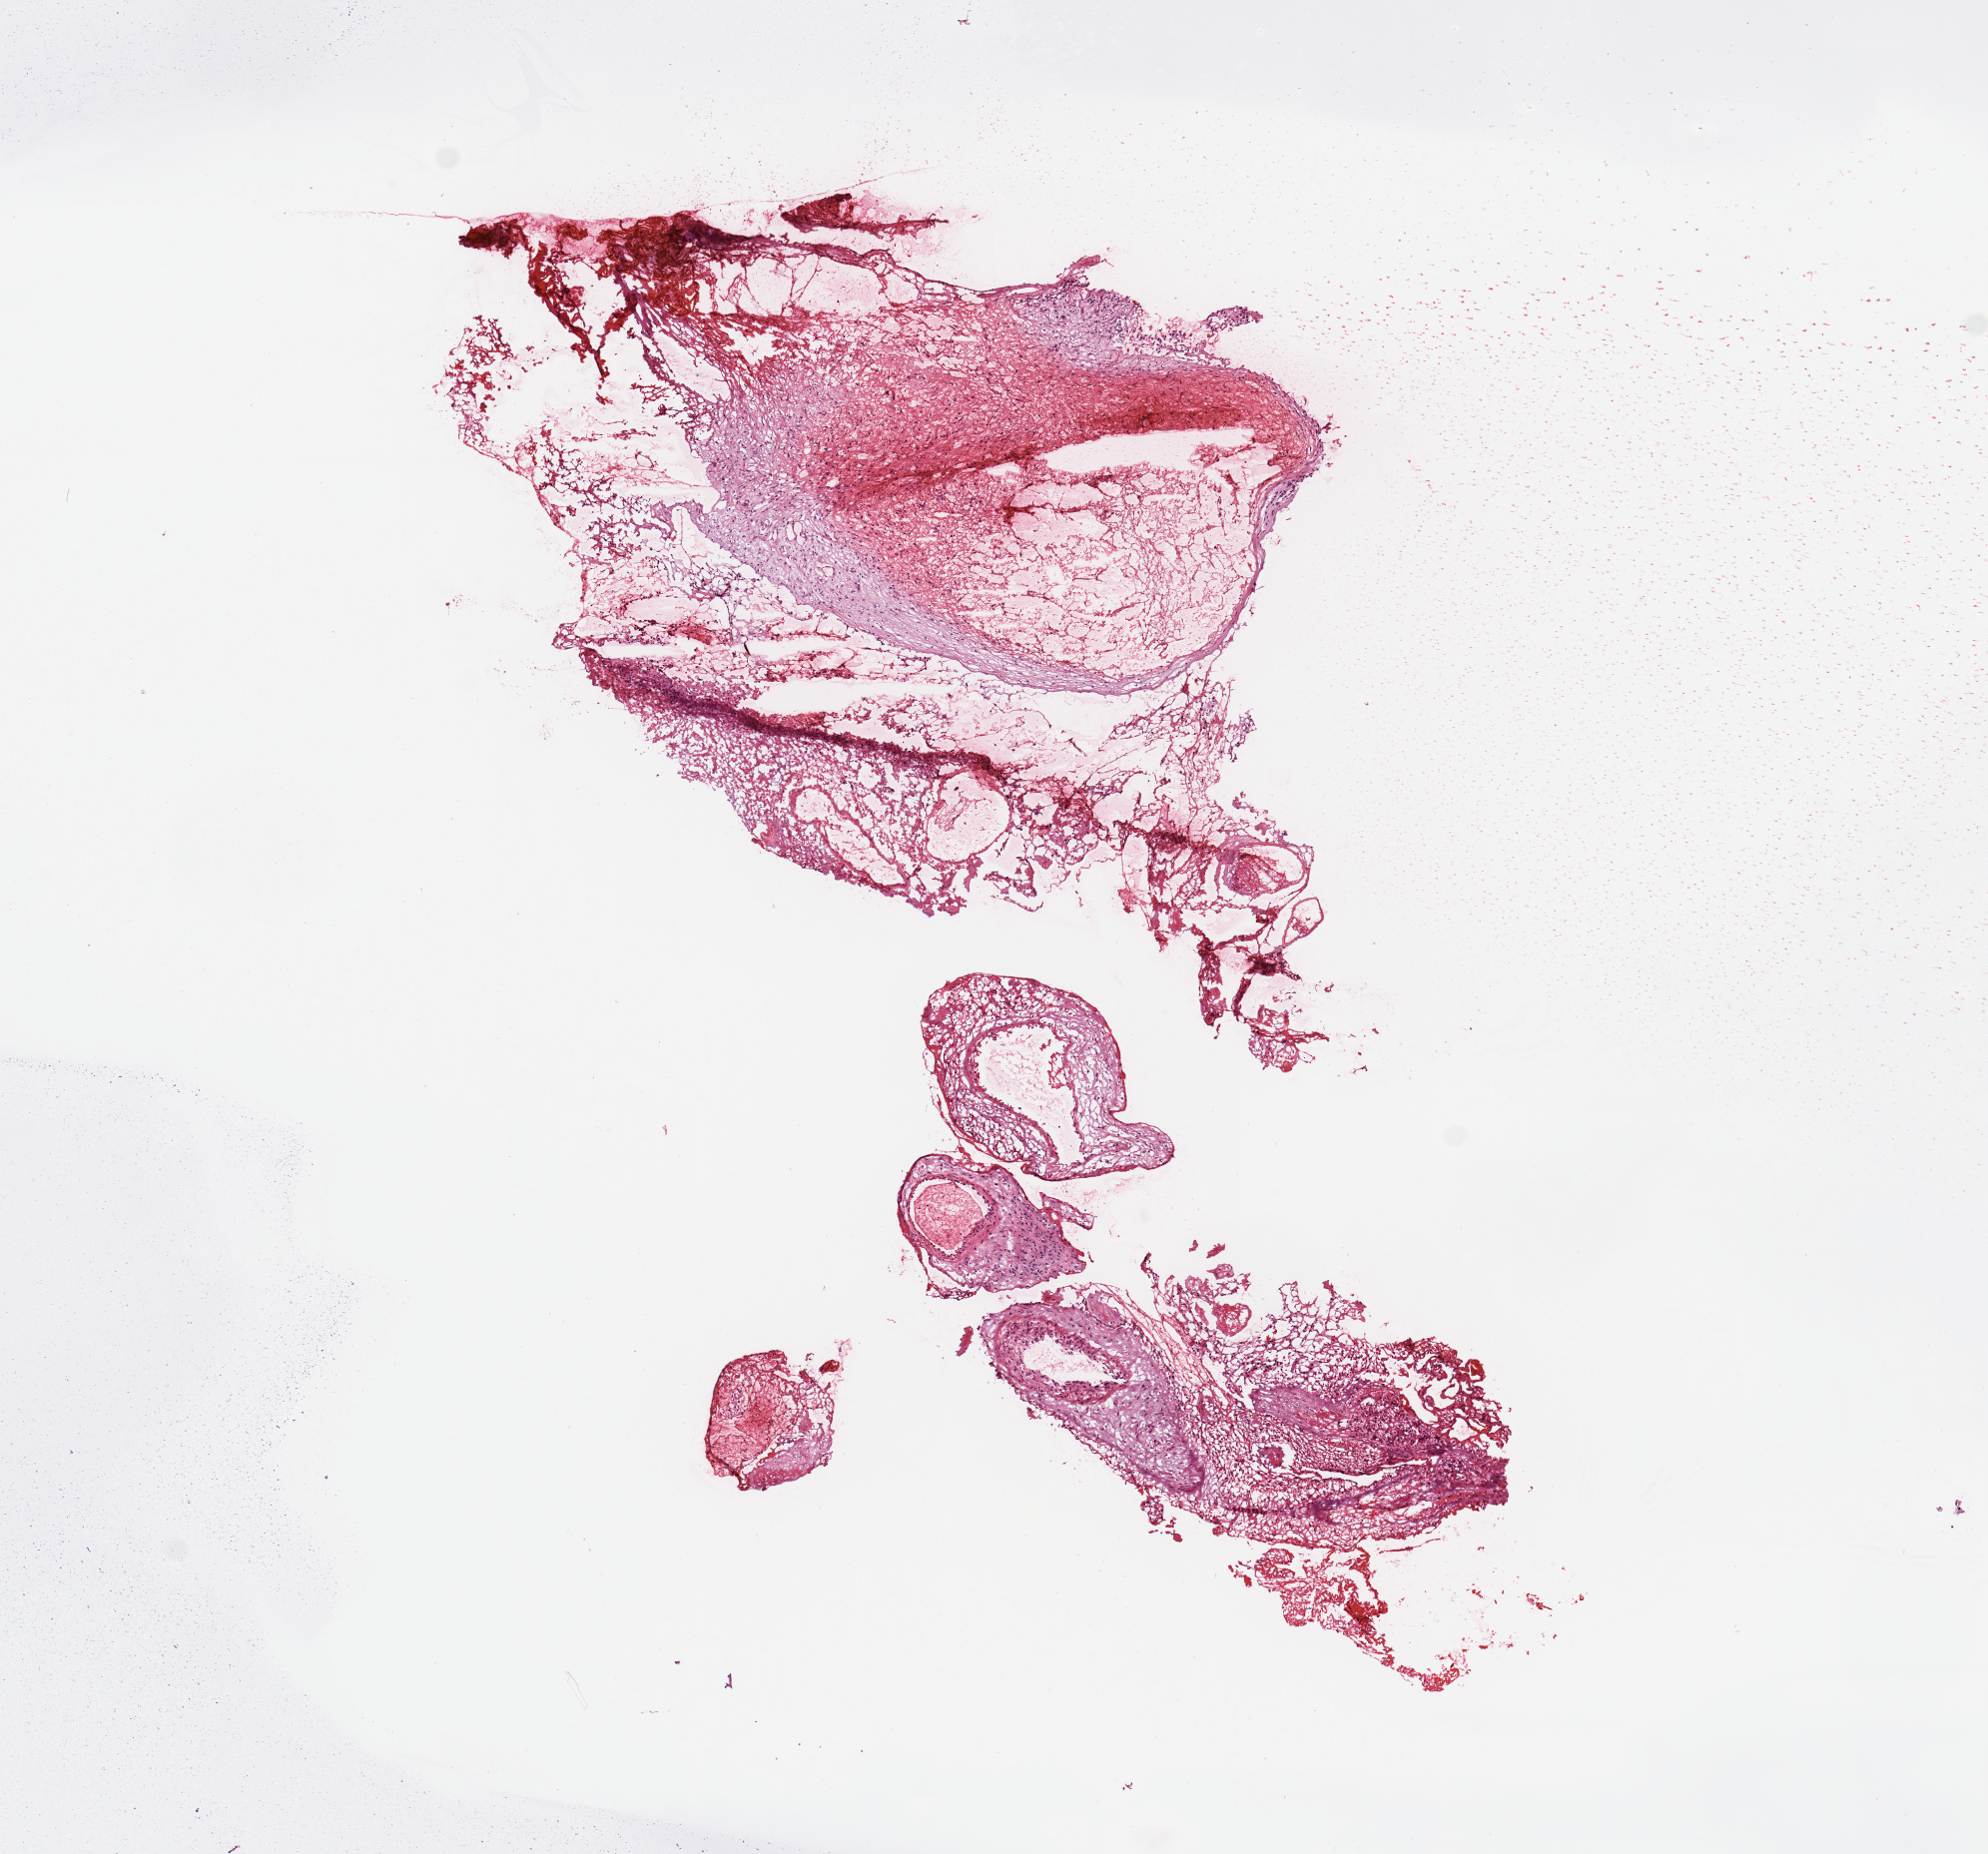
Digitized H&E tissue section (whole slide) — whole scanned area (about 7.9 x 7.3 mm) shown as a low-resolution overview. Brain, tumour tissue. Male, 61 y/o.
Patient diagnosis (cohort enrolment): glioblastoma multiforme (brain). Primary tumour site (as recorded): frontal lobe.